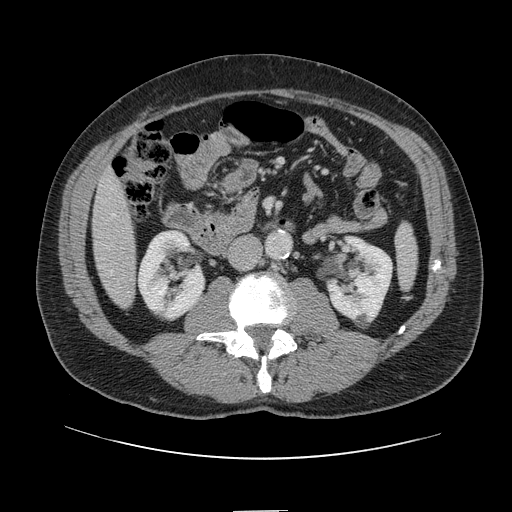
Contrast-enhanced abdominal CT, one axial slice. Position 24 of 161 along the scan axis. Soft-tissue window (W 400 / L 40 HU). 2.5 mm slice thickness. 512 × 512 image matrix, field of view 412 × 412 mm. Male patient, age 66 years. From the clinical record (not read from this slice): diagnosis: colorectal cancer liver metastases, imaged before liver resection; multiple liver metastases: no; largest metastasis: 3.5 cm; disease in both lobes: no.
Outlined on this slice (expert manual segmentation):
- hepatic veins: box from (x=112, y=214) to (x=115, y=217) px
- liver: (x=93, y=171)–(x=135, y=307)
- planned liver remnant (the part of the liver to remain after resection): (x=93, y=171)–(x=132, y=255)